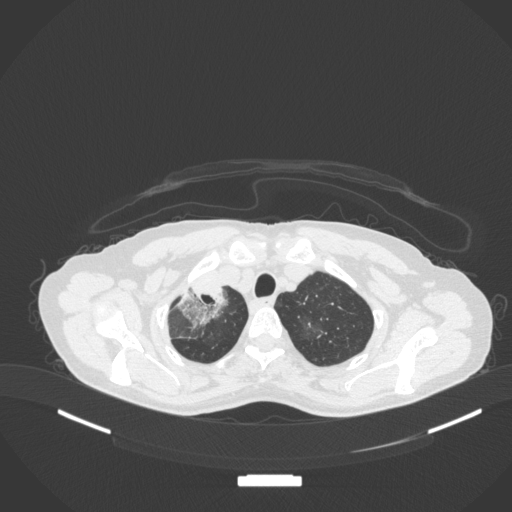
Chest CT, one axial slice. Position 282 of 311 along the scan axis. Reconstruction kernel B31f. 120 kVp. Lung window (W 1500 / L -600 HU). 1 mm slice thickness. 512 × 512 image matrix, field of view 400 × 400 mm. Female patient, age 59 years. Case-level facts recorded for this patient, not image findings: clinical TNM (as recorded): T3 N0 M0; histopathological grade: G1.
Outlined on this slice (rectangle marked by the reading radiologist):
- lung tumour (recorded histology: adenocarcinoma): bounding box <173,278,232,333> (left, top, right, bottom; pixels)